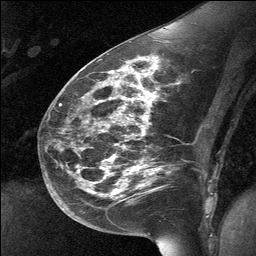
Breast MRI (dynamic contrast-enhanced), one sagittal slice; position 30 of 64 along the scan axis; dynamic contrast-enhanced study with each time point stored as its own series, time point 2 of 3 at this slice position (early post-contrast, ordered by acquisition time); 1.5 T; TE 4.8 ms, TR 27 ms; 2 mm slice thickness; 256 × 256 image matrix, field of view 200 × 200 mm. Patient: female, 39 years. Case-level facts recorded for this patient, not image findings: setting: breast cancer imaged before/during neoadjuvant chemotherapy; receptor status: HER2-positive.
Annotated regions visible in this slice (semi-automatically segmented with operator editing):
- analysis volume of interest (the breast-tissue region the enhancement analysis was run in; not a lesion): bounding box [x1, y1, x2, y2] px = [70, 69, 158, 224]
- tumour enhancement mask (voxels above the 90 % enhancement threshold inside the analysis volume of interest): [124, 69, 127, 71]